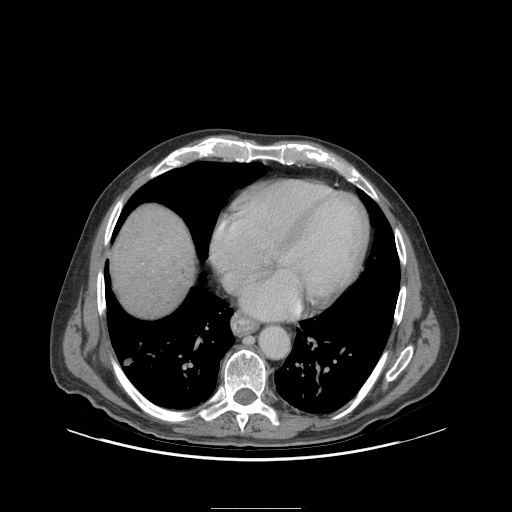
Contrast-enhanced abdominal CT (liver protocol), one axial slice; slice 94 of 105 in the series (ordered by position); reconstruction kernel STANDARD; 140 kVp; soft-tissue window (W 400 / L 40 HU); 2.5 mm slice thickness; 512 × 512 image matrix. From the clinical record (not read from this slice): diagnosis: hepatocellular carcinoma (patient treated with transarterial chemoembolisation; whether this scan precedes or follows treatment is not stated here); TNM stage (as recorded): Stage-I; Child-Pugh class: A; tumour size: 5.1 cm.
Structures marked on this image (semi-automatic segmentation, software-assisted and operator-edited):
- liver parenchyma outside the tumour (the mass and vessels are separate outlines, so this box may not span the whole liver): bounding box <110,204,194,316> (left, top, right, bottom; pixels)